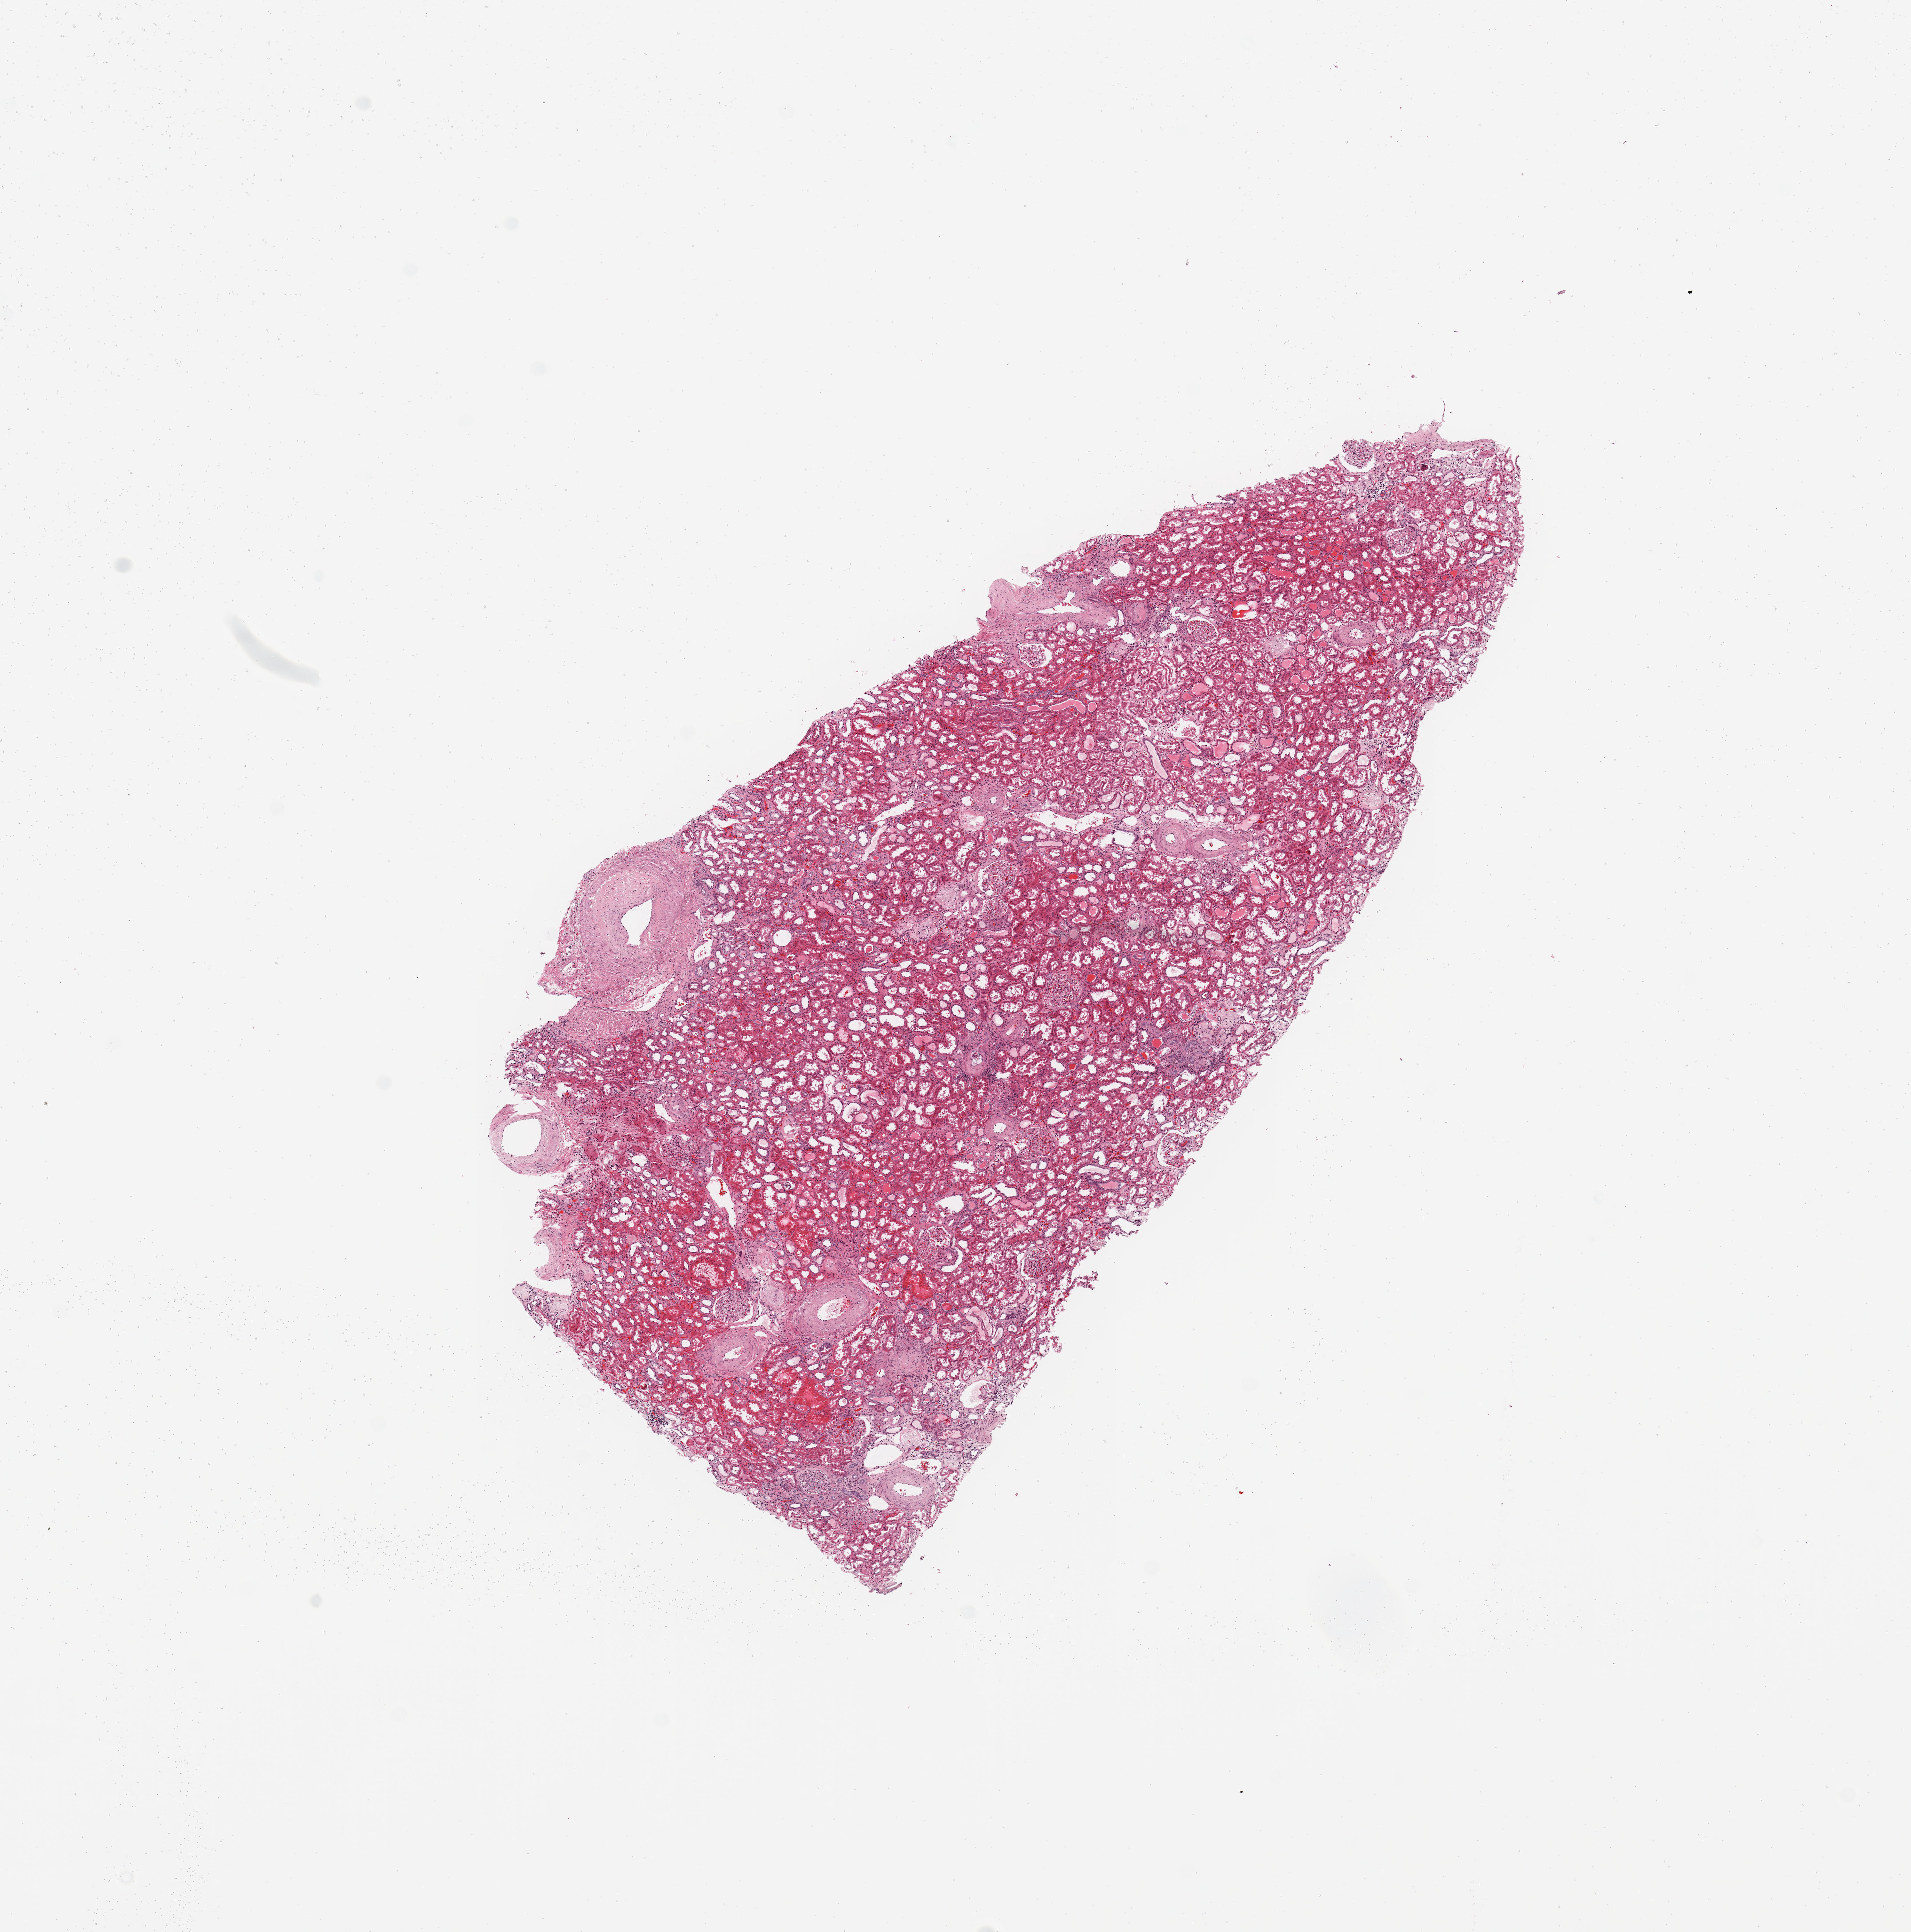
Digitized Hematoxylin and eosin (H&E) stained tissue section (whole slide) — whole scanned area (about 11.8 x 11.9 mm) shown as a low-resolution overview, normal (non-tumour) tissue sample, sampled site: kidney. Patient: male, age 58 years.
This section: normal (non-tumour) tissue from the same patient. Patient diagnosis: Renal cell carcinoma, NOS.